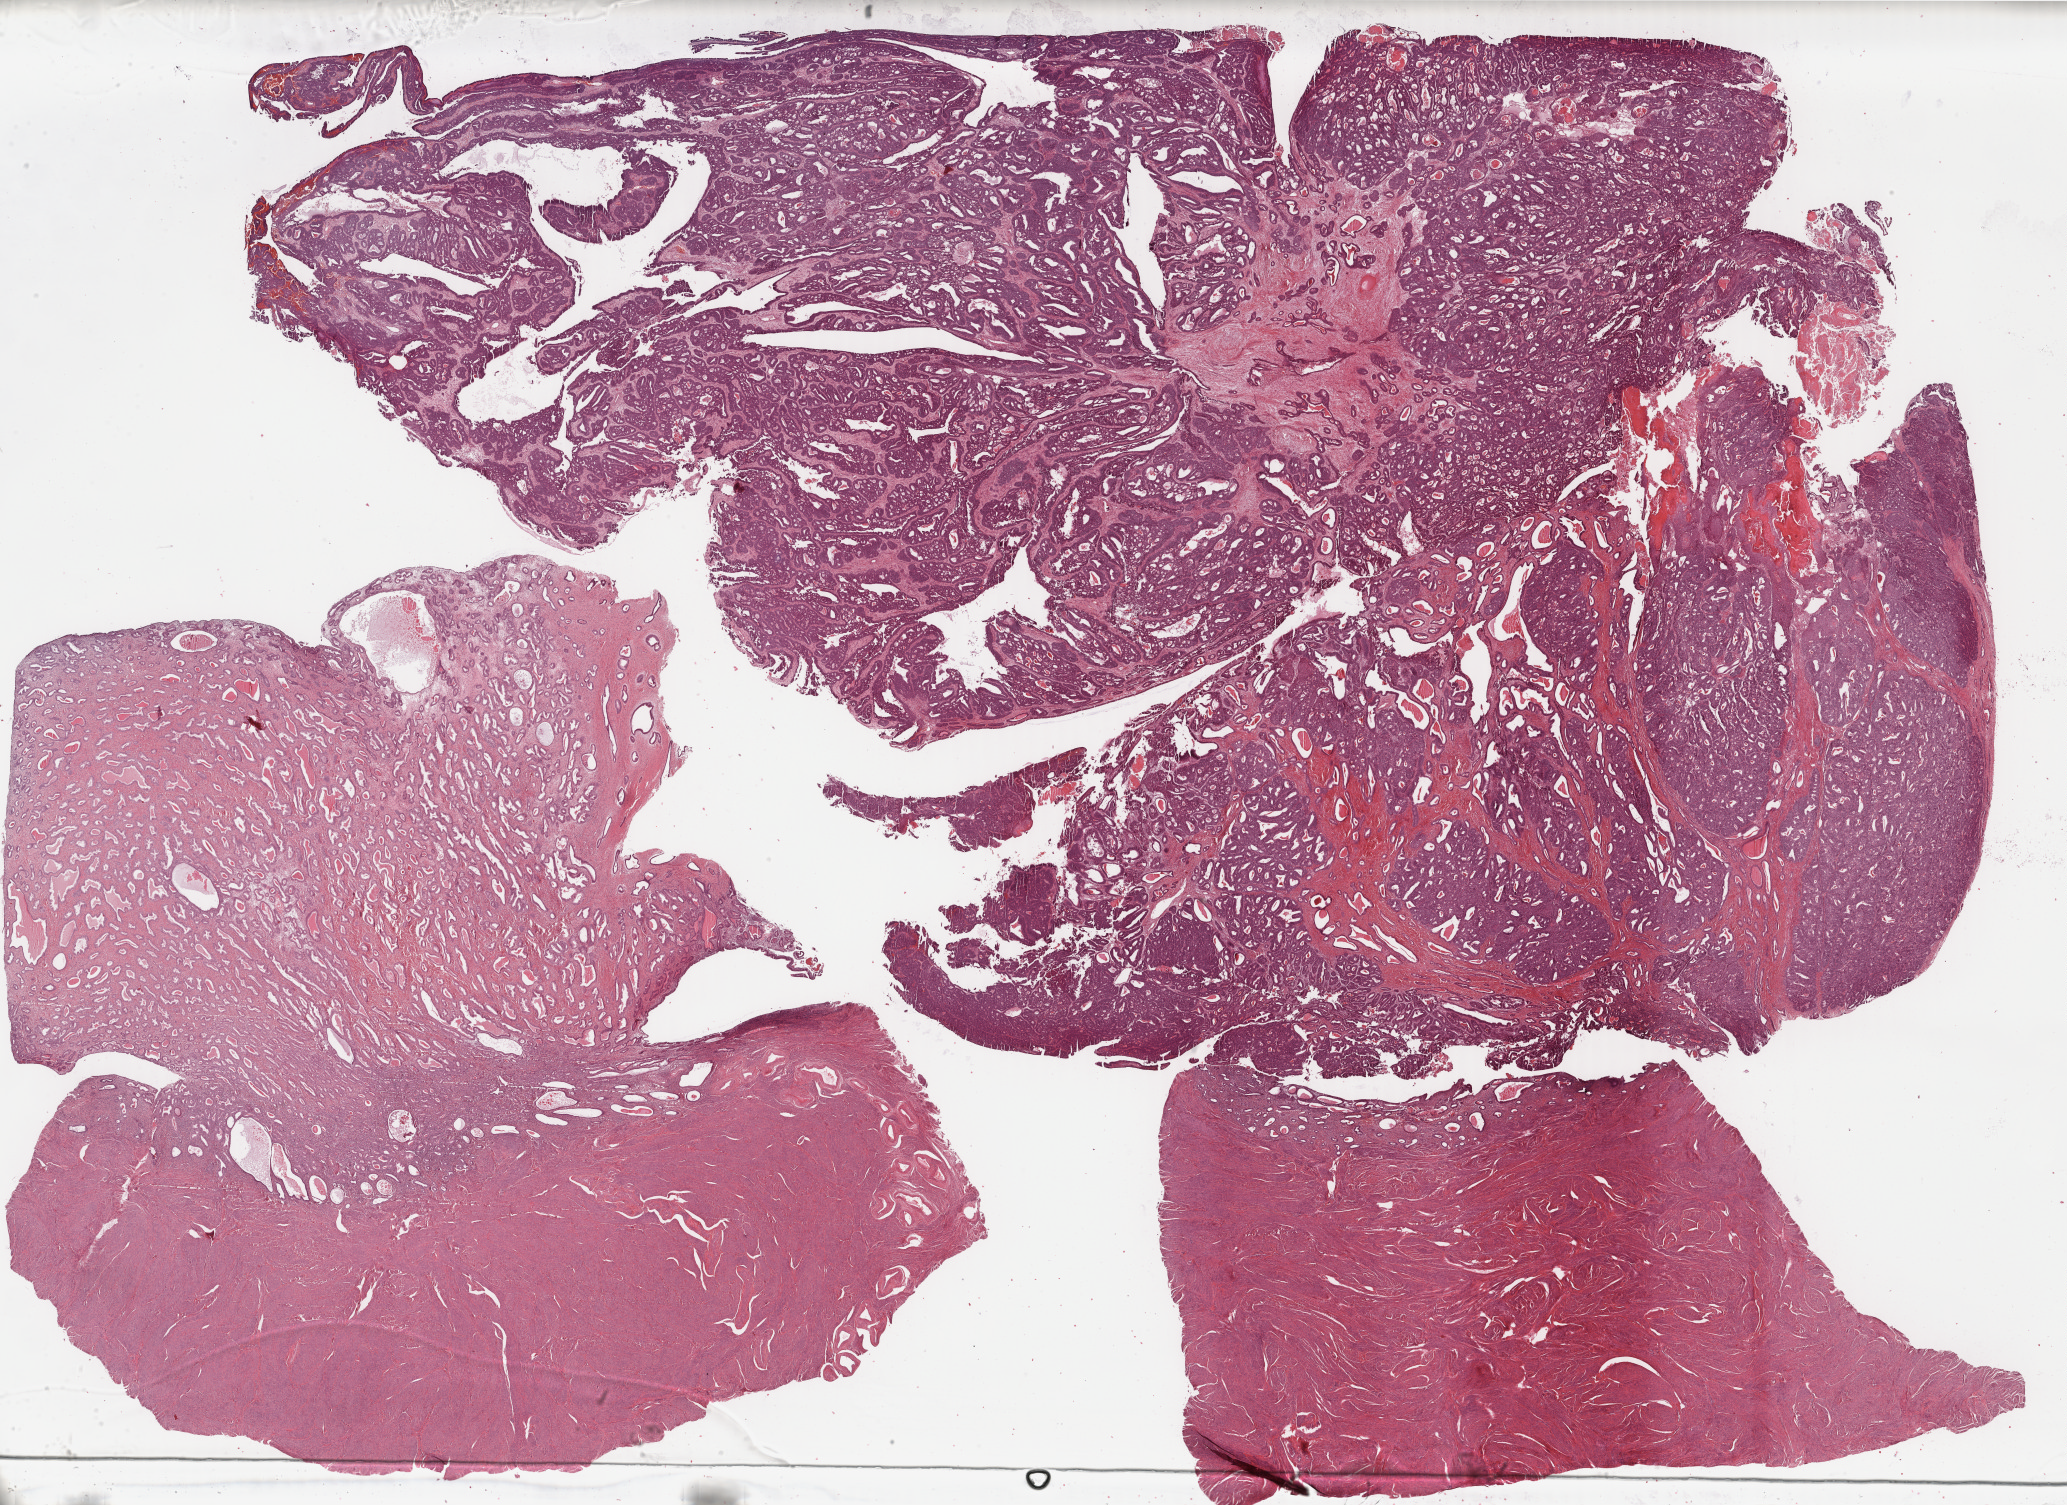
Digitized H&E-stained tissue section (whole slide) — shown as a low-resolution overview of the whole scanned area (about 32.8 x 23.9 mm). FFPE section. Uterus, primary tumour sample. Female, age 55 years at initial diagnosis. Histologic grade: G2 (moderately differentiated).
Pathologic diagnosis: Endometrioid adenocarcinoma, NOS (endometrium). FIGO stage: IA.